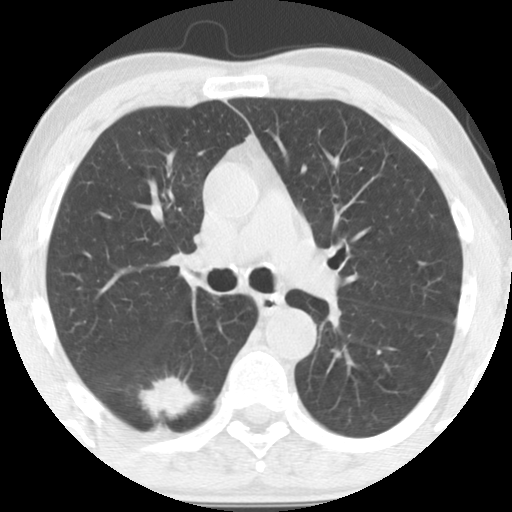
Axial slice from a low-dose chest CT screening exam; baseline annual screen; lung window (W 1500 / L -600 HU); 2.5 mm slice thickness; slice 47 of 135 in the series; 512 × 512 image matrix, field of view 300 × 300 mm. Male, age 64 years at enrolment.
- Expert reader's lesion annotation, bounding box (x1, y1, x2, y2) in pixels: (119, 366, 194, 433).
- The exam's reader record, not a measurement of the box and not confirmed to be the same lesion: non-calcified nodule or mass ≥4 mm, right lower lobe, 36 × 26 mm, spiculated (stellate) margins, soft tissue attenuation.
- Official screen result: positive, change unspecified: nodule(s) >= 4 mm or enlarging nodule(s), mass(es), or other non-specific abnormalities suspicious for lung cancer.
- Lung cancer was diagnosed 20 days after this screen: adenocarcinoma, NOS, right lower lobe, moderately differentiated (G2), stage IA (AJCC 6th edition), 28 mm at pathology.